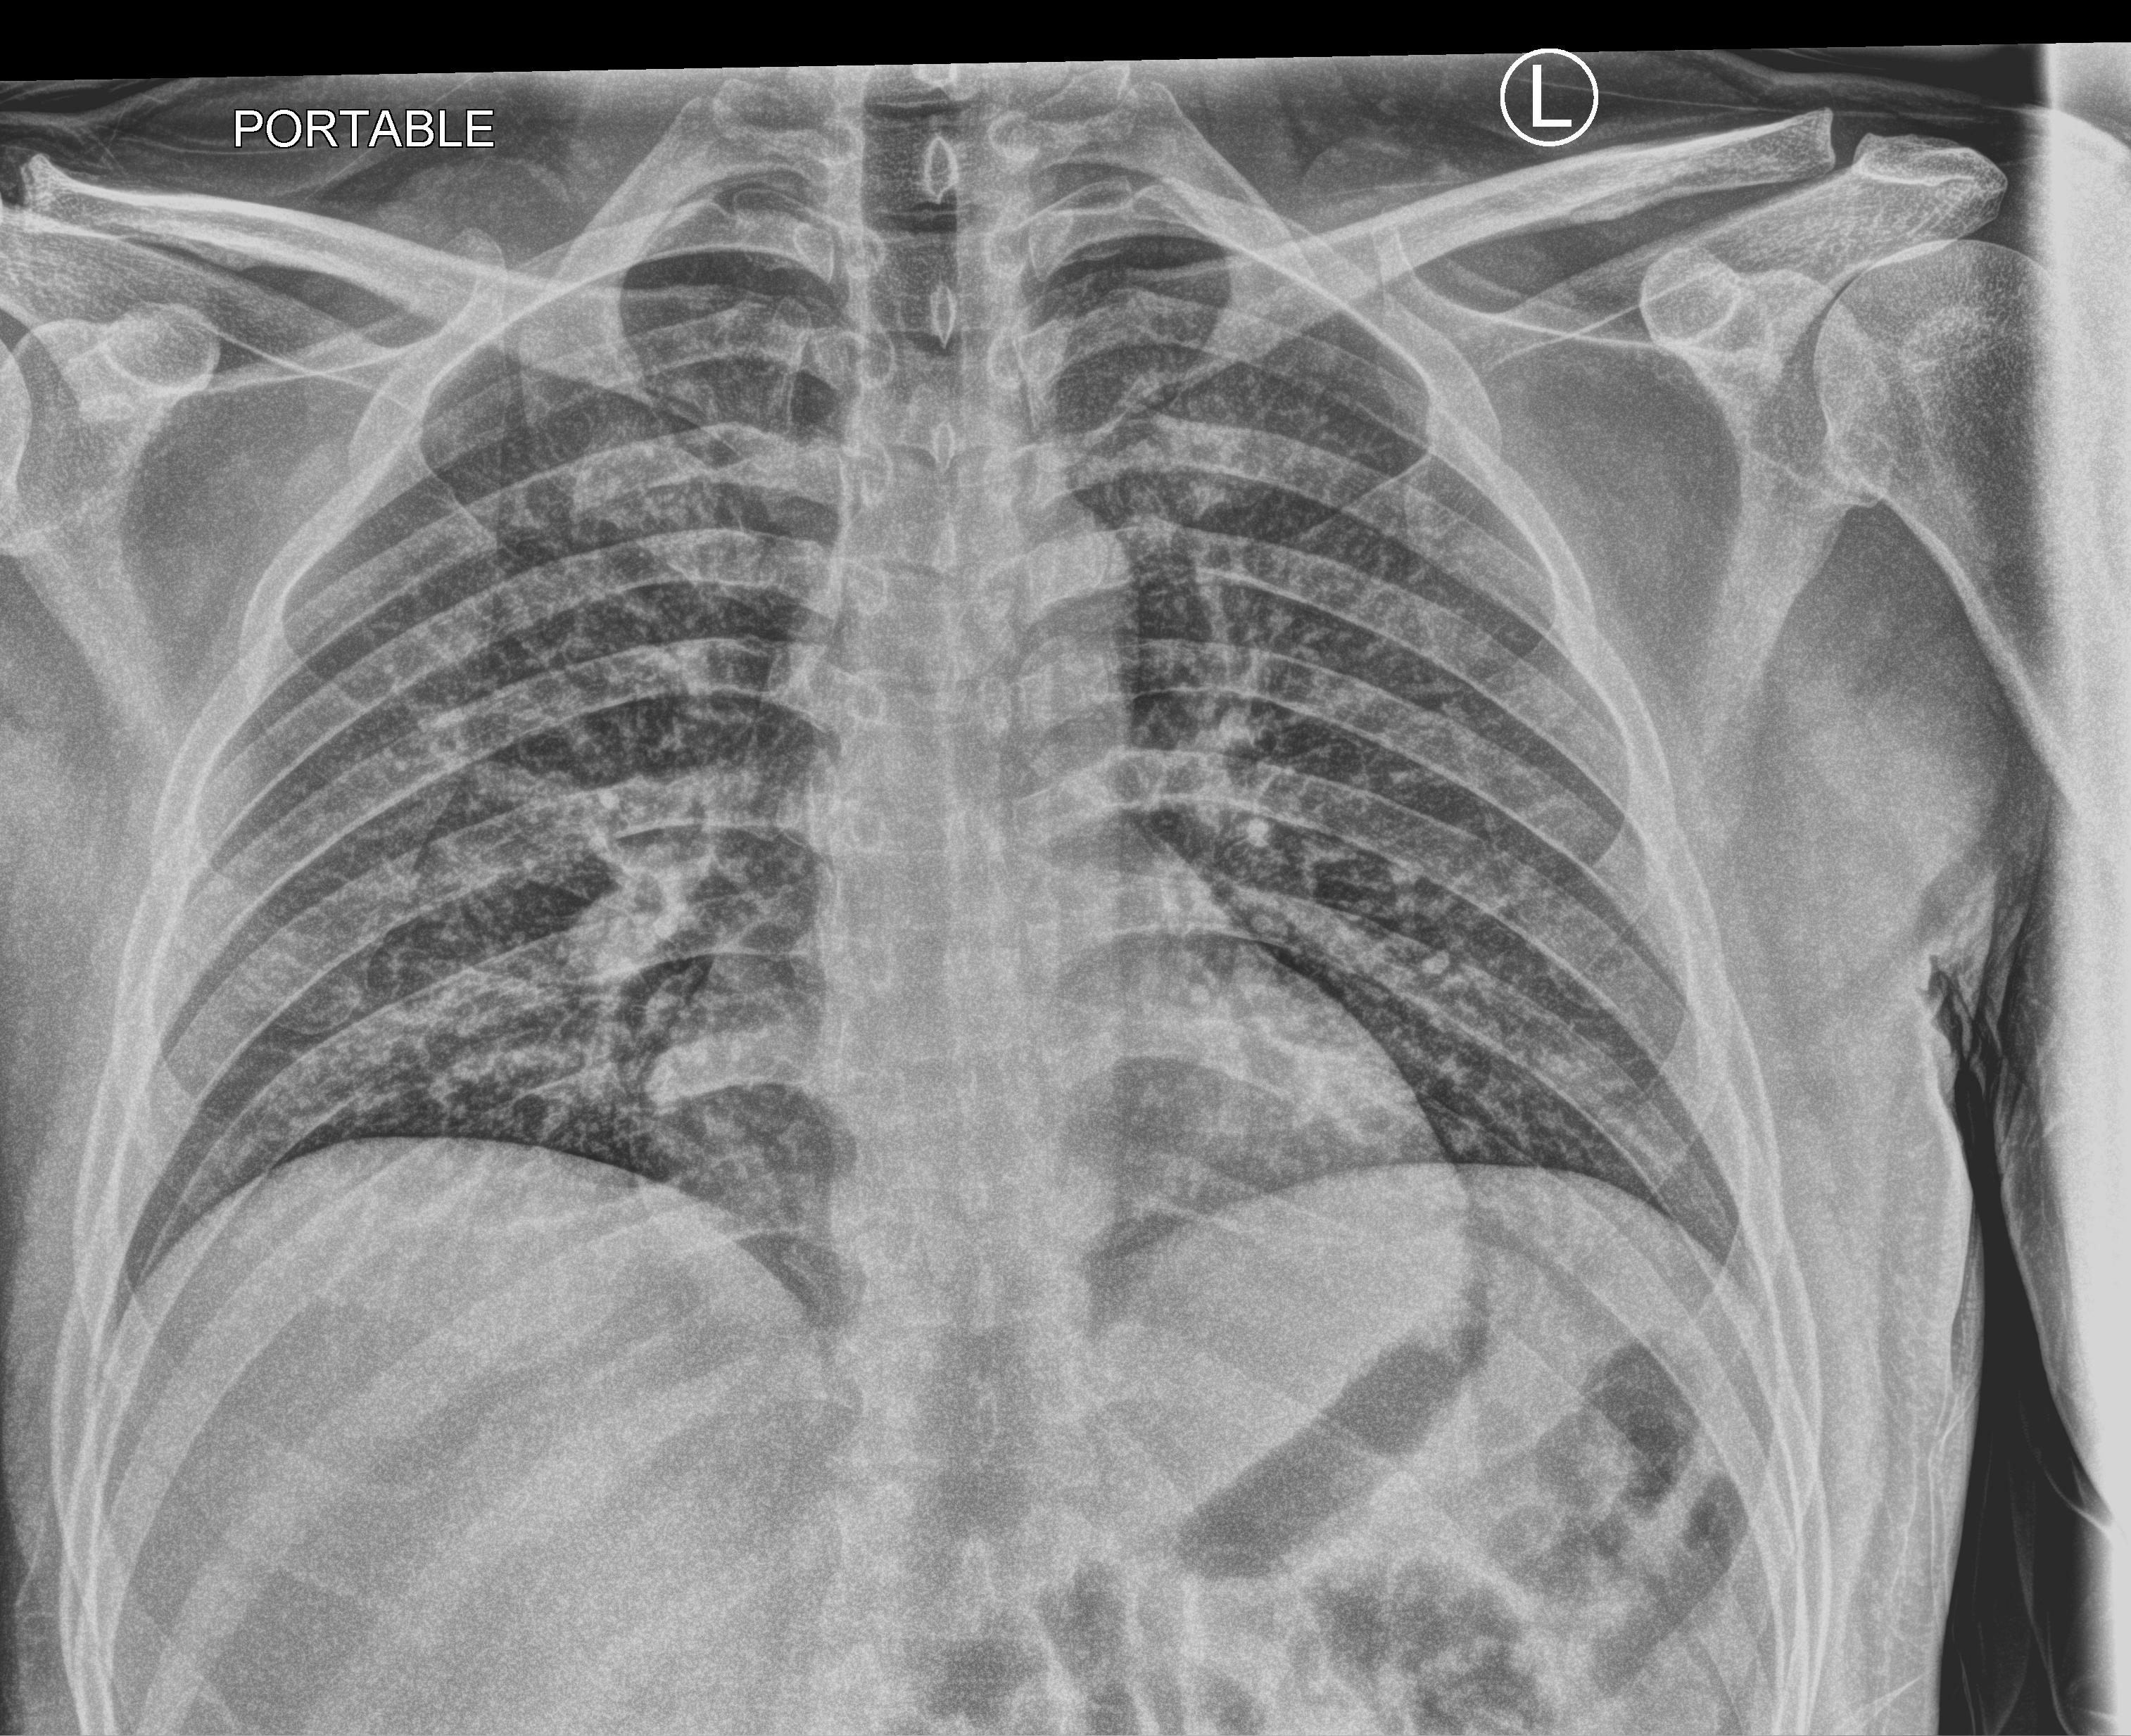
Portable chest radiograph; anteroposterior (AP) projection. Patient hospitalised with COVID-19; male, aged 18–59 years.
Admission-level facts for this patient (not findings on this image; timing relative to this image not recorded): mechanically ventilated during this hospital stay: no.